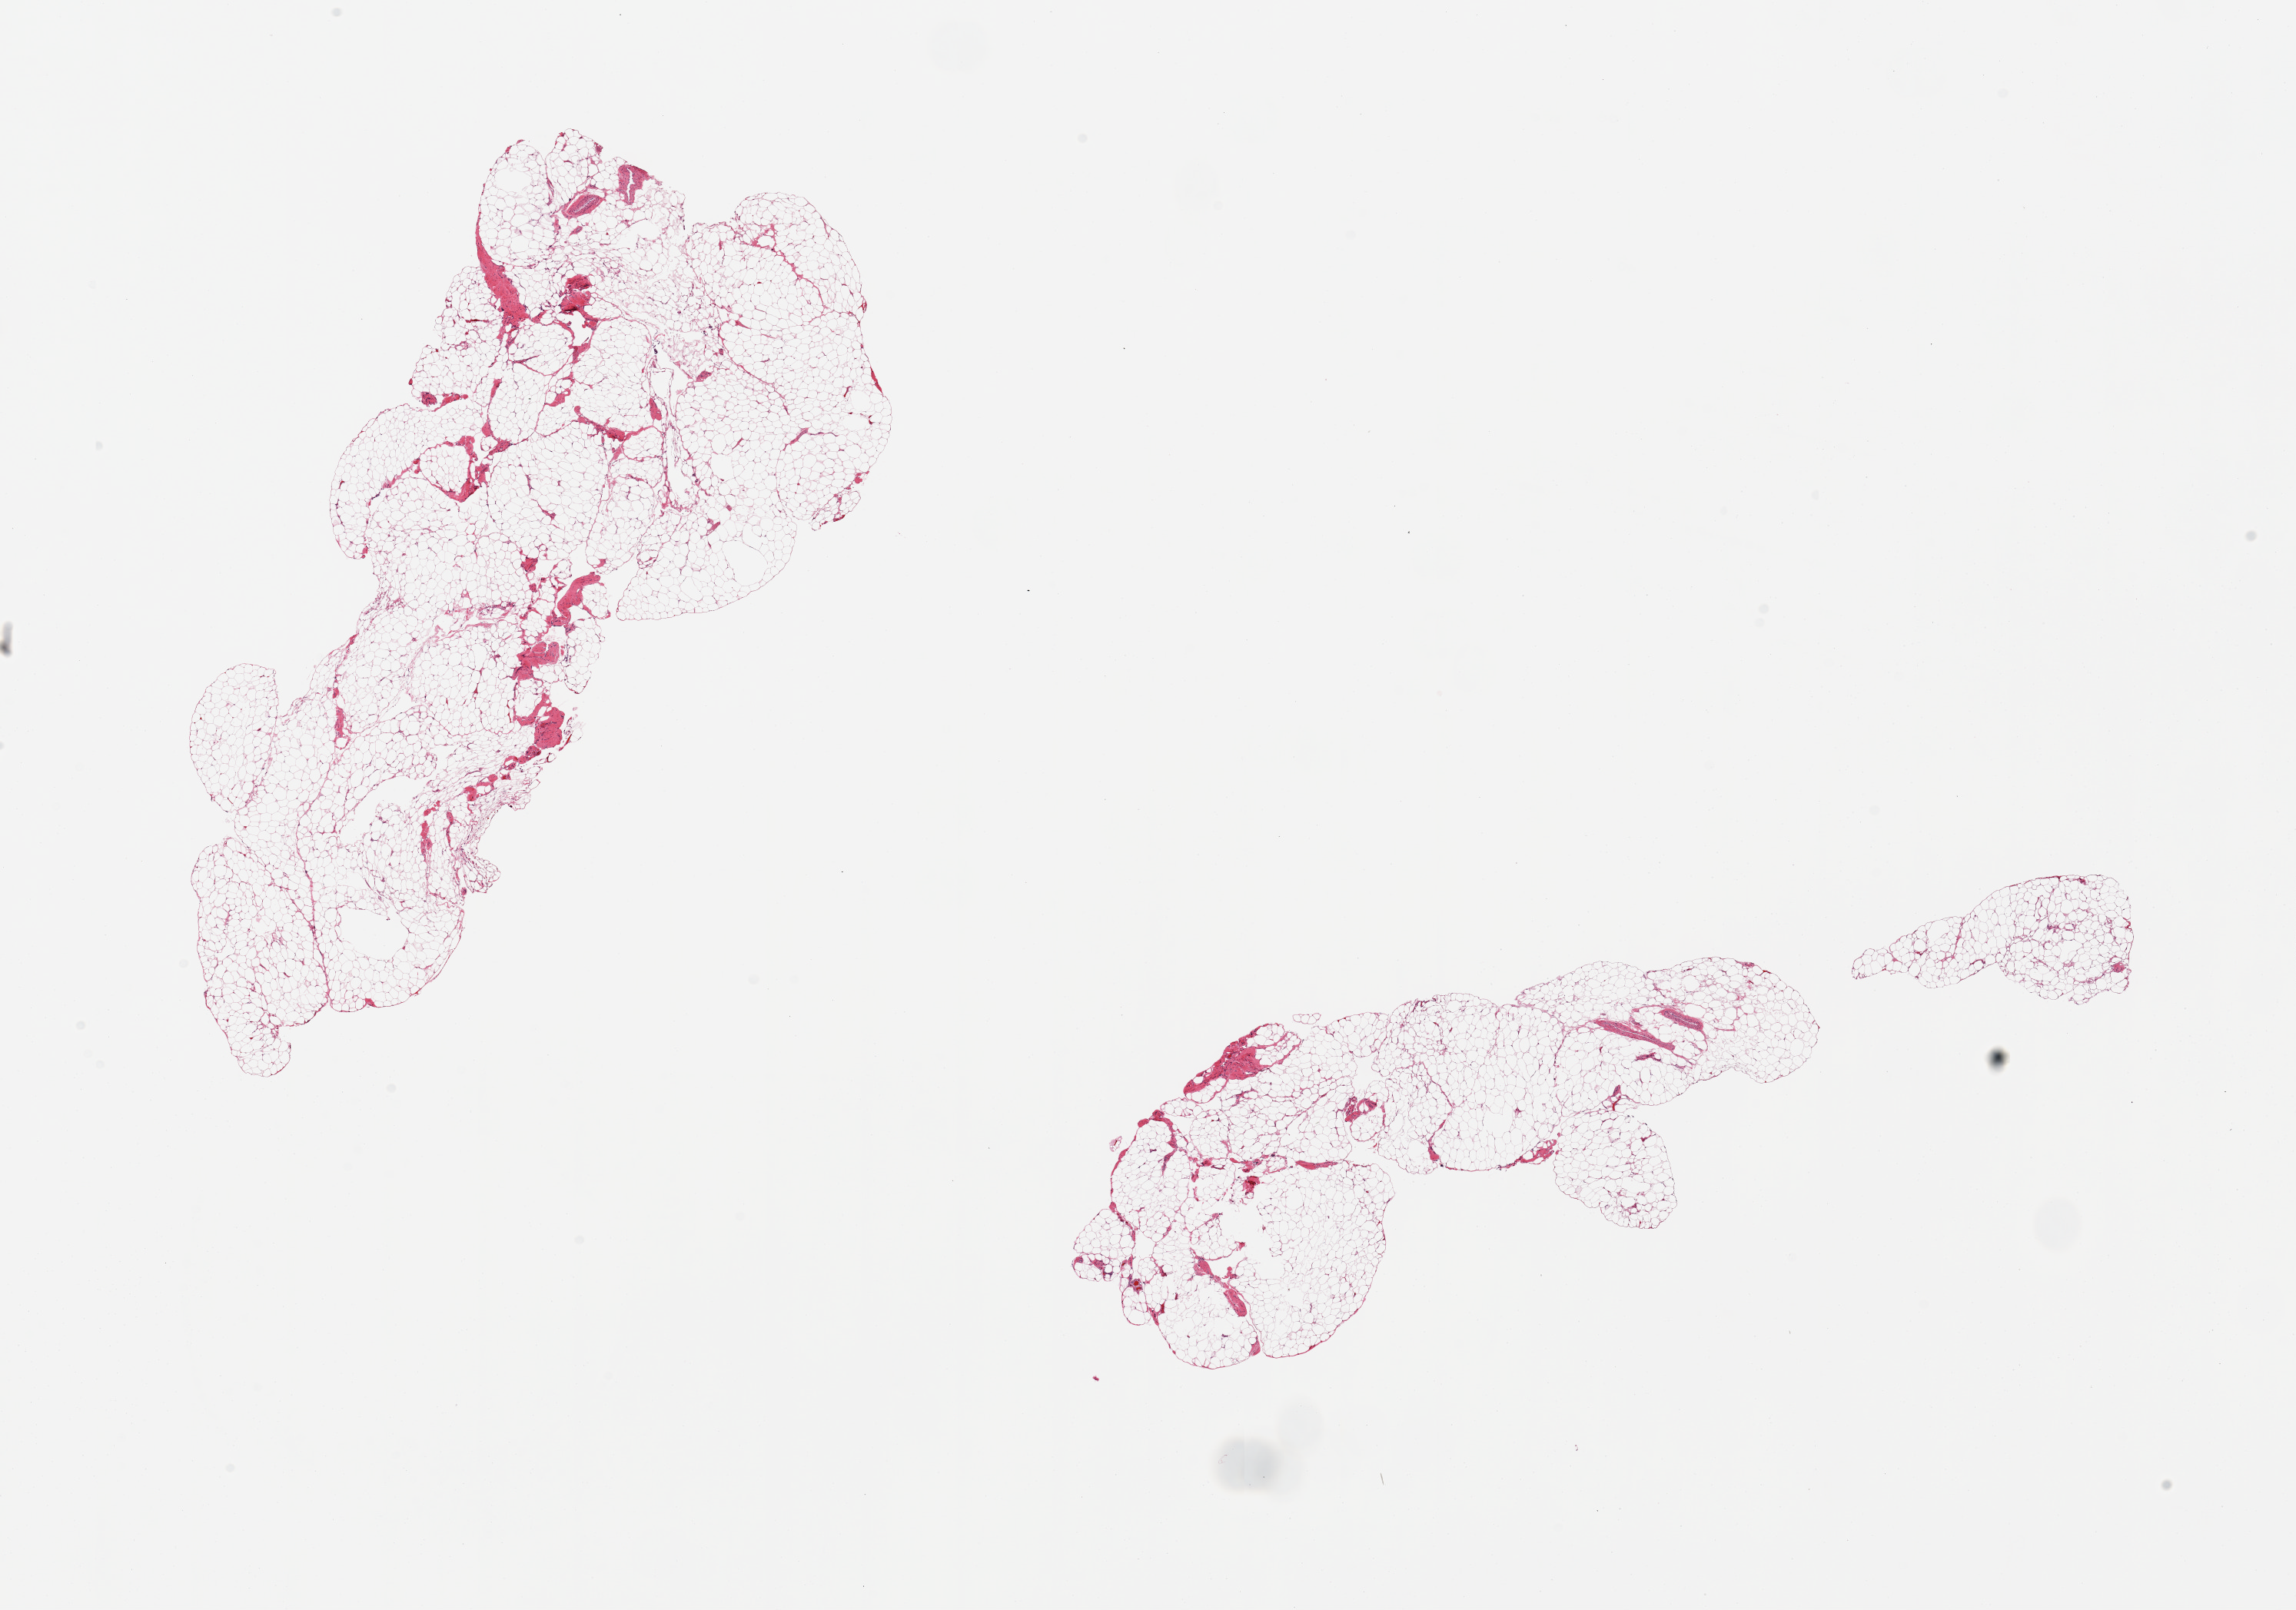
Whole-slide image, hematoxylin and eosin (H&E) stain, brightfield — whole scanned area (about 23.6 x 16.6 mm) shown as a low-resolution overview; PAXgene-fixed paraffin-embedded (PFPE) section; section of omentum (target tissue); donor tissue sample.
Reviewer comment on this tissue sample: 2 pieces; no increase in fibrous stroma.